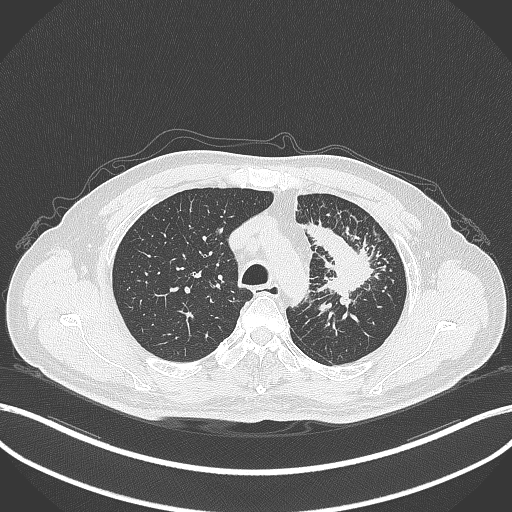
Chest CT, one axial slice; position 272 of 386 along the scan axis; 120 kVp; lung window (W 1500 / L -600 HU); 1 mm slice thickness; 512 × 512 image matrix, field of view 400 × 400 mm. Patient: male, 69 years. Case-level facts recorded for this patient, not image findings: clinical TNM (as recorded): T2a N2 M0; histopathological grade: G2-3.
Structures marked on this image (rectangle marked by the reading radiologist):
- lung tumour (recorded histology: adenocarcinoma): bounding box <298,218,382,300> (left, top, right, bottom; pixels)